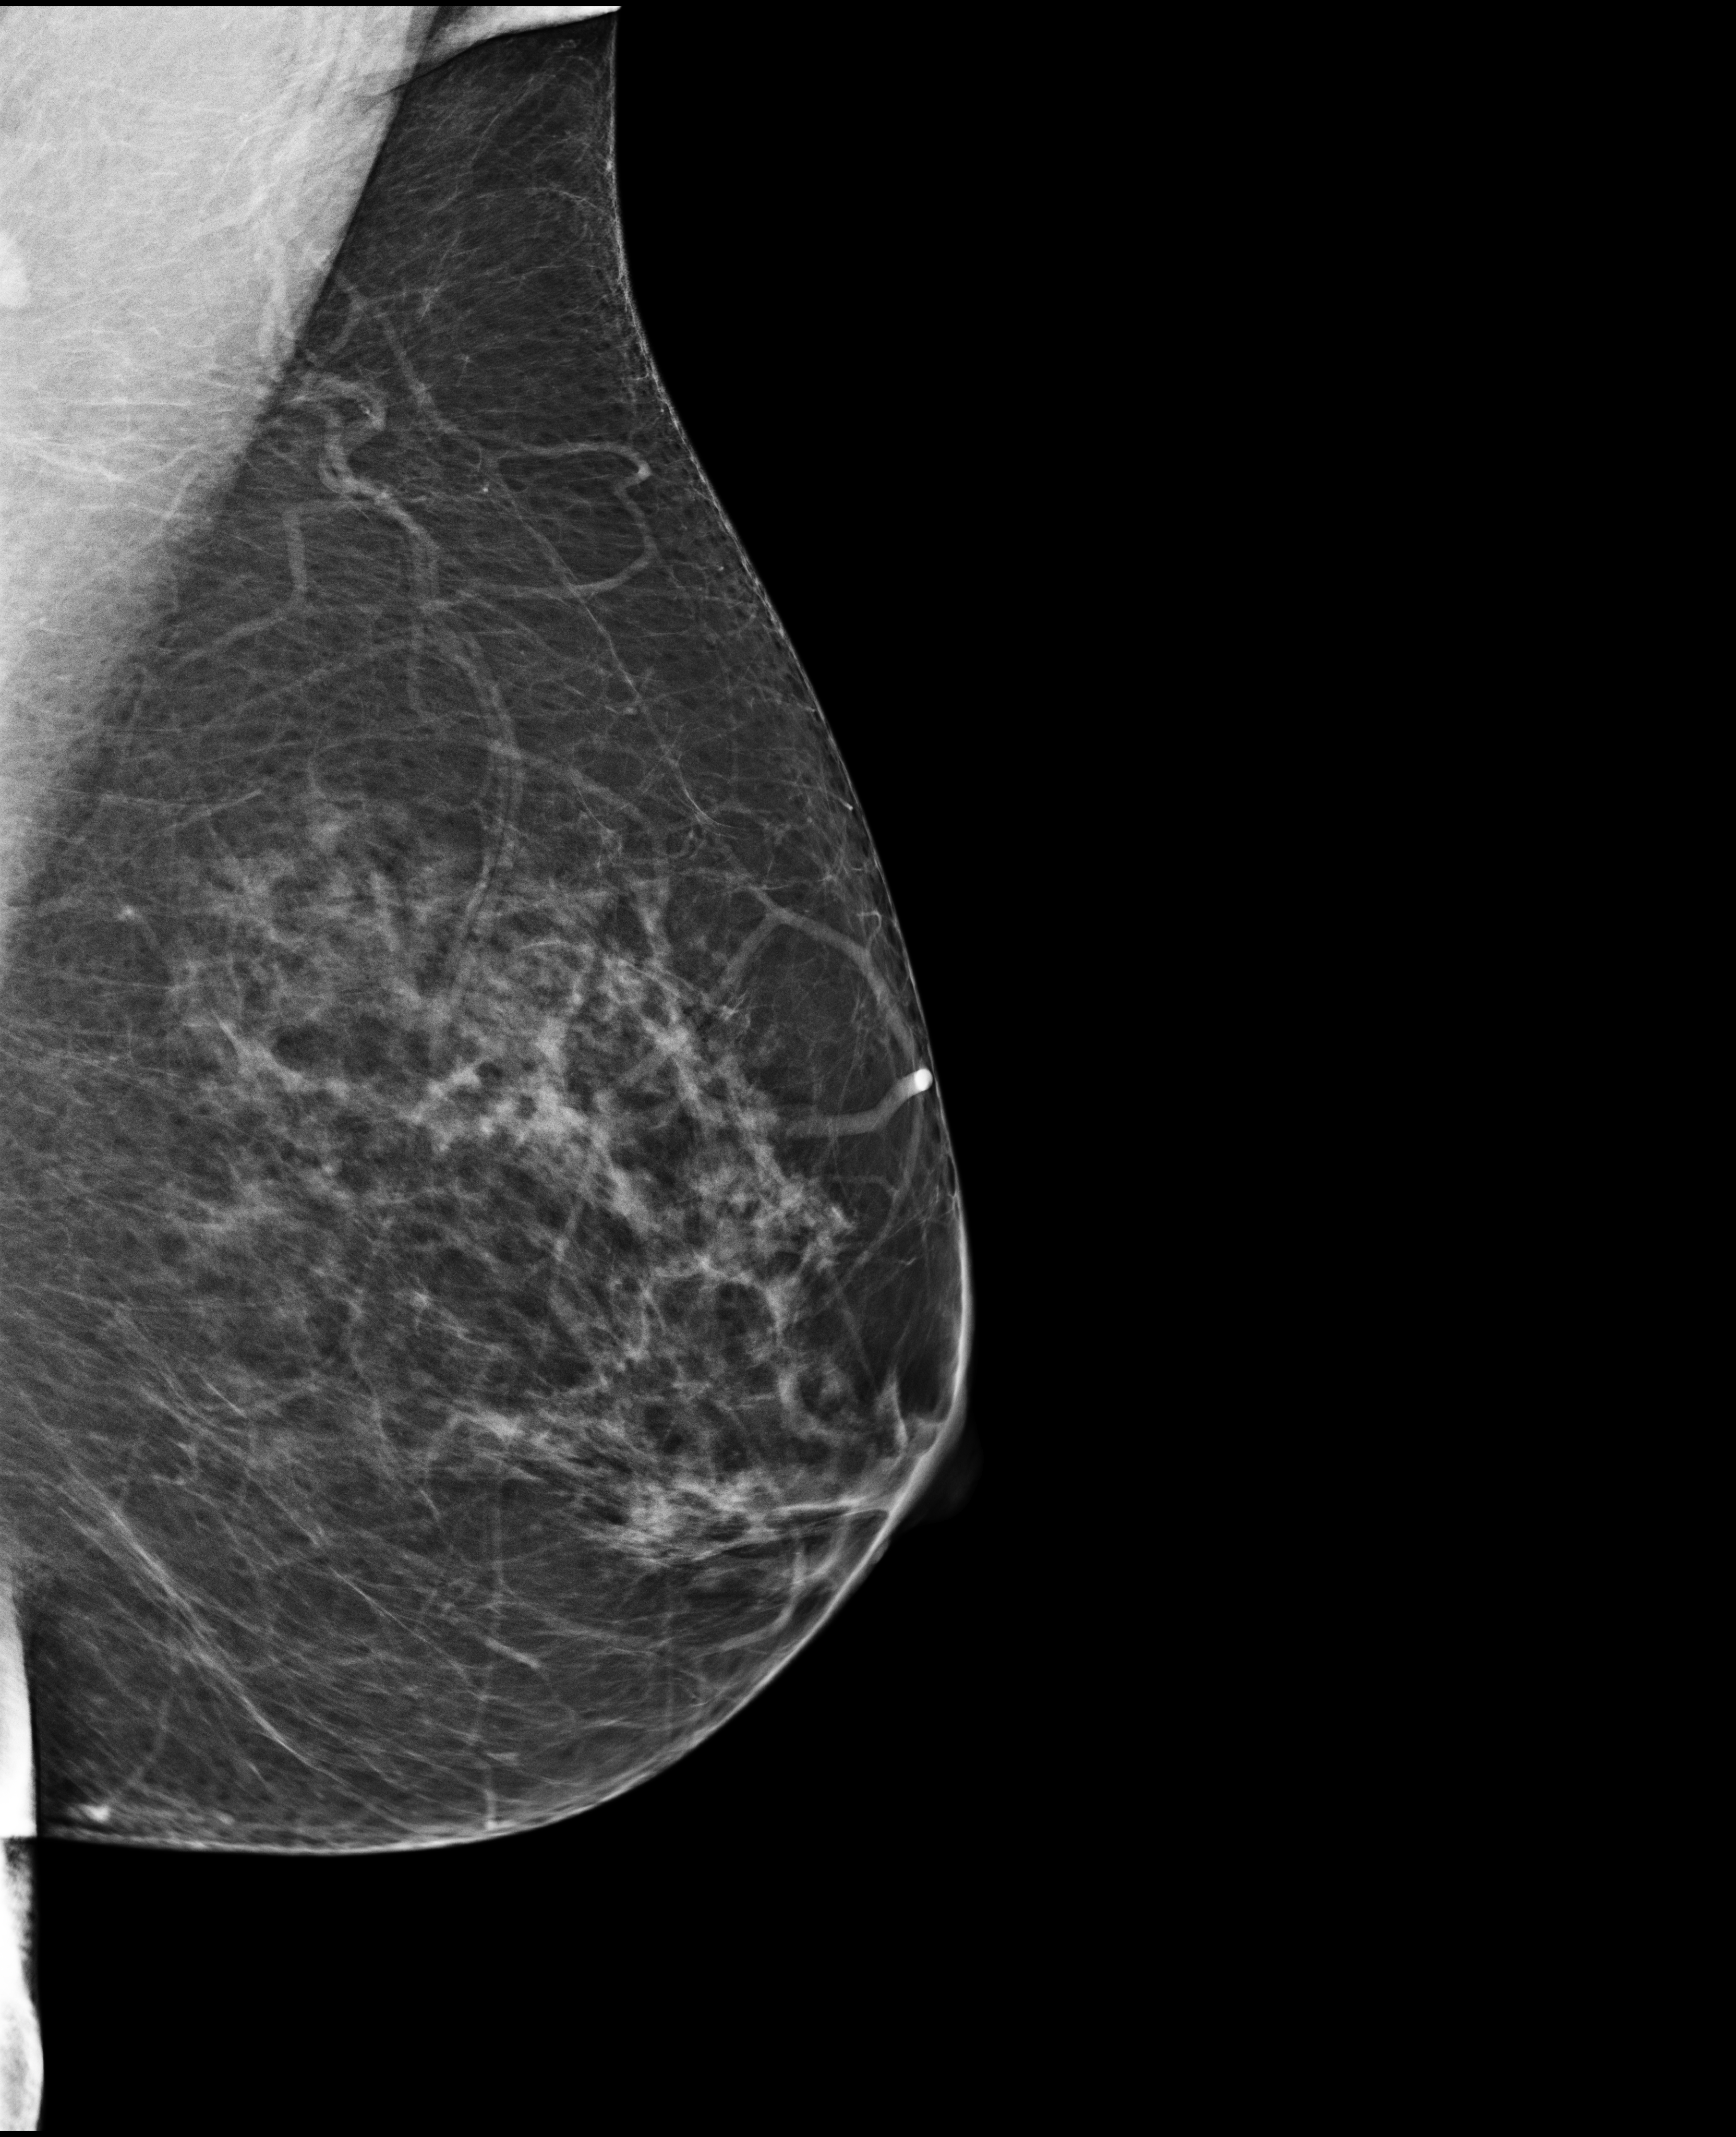
Annual screening mammography examination; compressed breast thickness 85 mm; system: Selenia Dimensions. Patient: female, 60 years.
Image type: full-field digital mammogram. Breast: left. Projection: mediolateral oblique (MLO) view.